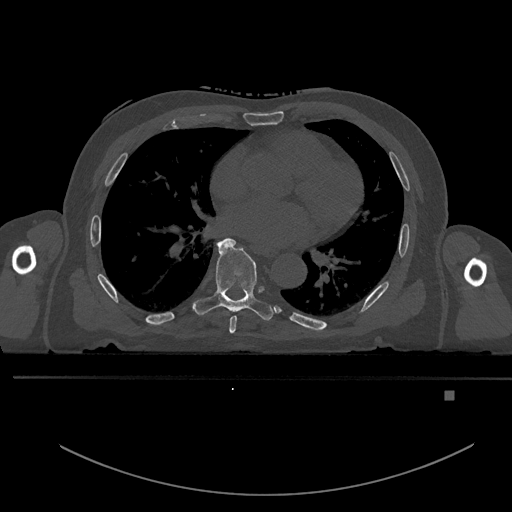
CT including the spine, one axial slice. Position 262 of 969 along the scan axis. Bone window (W 1800 / L 400 HU). 0.5 mm slice thickness. 512 × 512 image matrix, field of view 456 × 456 mm. Male patient, age 82 years. From the clinical record (not read from this slice): primary cancer: prostate.
Annotated regions visible in this slice (semi-automatically segmented with operator editing):
- T6 vertebra: bounding box [x1, y1, x2, y2] px = [229, 315, 237, 334]
- T7 vertebra: [192, 238, 273, 321]